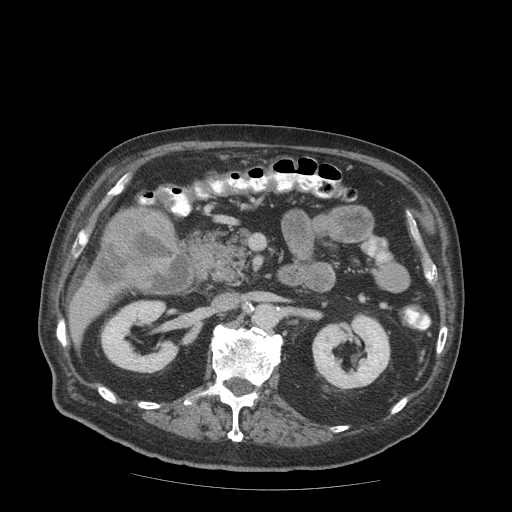
Contrast-enhanced abdominal CT (liver protocol), one axial slice; slice 27 of 99 in the series (ordered by position); reconstruction kernel STANDARD; soft-tissue window (W 400 / L 40 HU); 512 × 512 image matrix. Case-level facts recorded for this patient, not image findings: diagnosis: hepatocellular carcinoma (patient treated with transarterial chemoembolisation; whether this scan precedes or follows treatment is not stated here); TNM stage (as recorded): Stage-IIIB; Child-Pugh class: A; tumour differentiation: well differentiated; tumour nodularity: multinodular.
Outlined on this slice (semi-automatically segmented with operator editing):
- liver parenchyma outside the tumour (the mass and vessels are separate outlines, so this box may not span the whole liver): bounding box [x1, y1, x2, y2] px = [68, 206, 176, 344]
- mass: [92, 207, 179, 287]